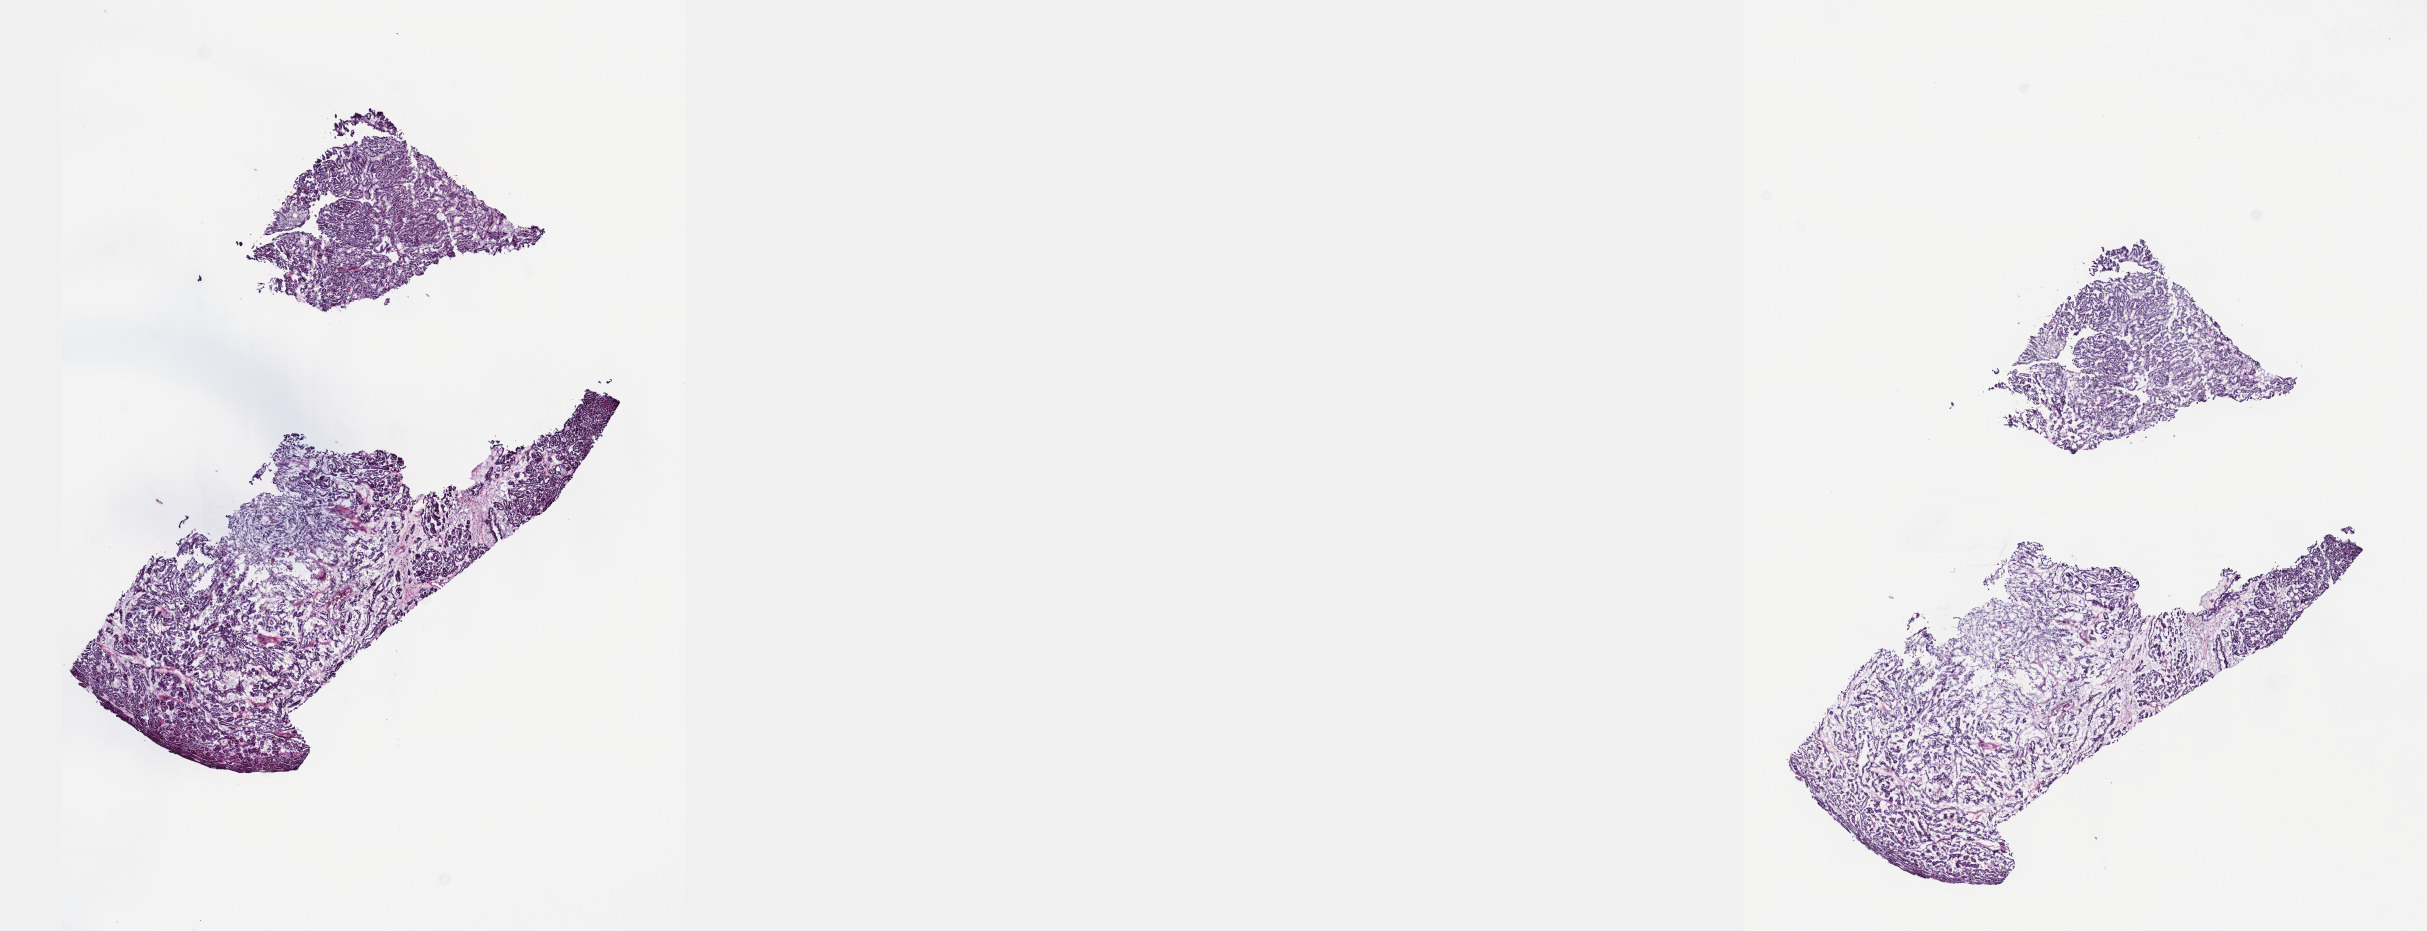
H&E whole-slide image, low-resolution overview of the scanned area, about 19.6 x 7.5 mm, frozen section from the top of the tissue portion, primary tumour sample from the kidney. Male, age 74 years at initial diagnosis. Pathologist review of this section (percent, as recorded): tumour cells 100%, tumour nuclei 80%, normal cells 0%, stromal cells 0%, necrosis 0%. Inflammatory infiltration, as recorded: lymphocyte infiltration 1%, monocyte infiltration 0%, neutrophil infiltration 0%.
- AJCC pathologic stage: I
- pathologic diagnosis: Papillary adenocarcinoma, NOS
- laterality: left